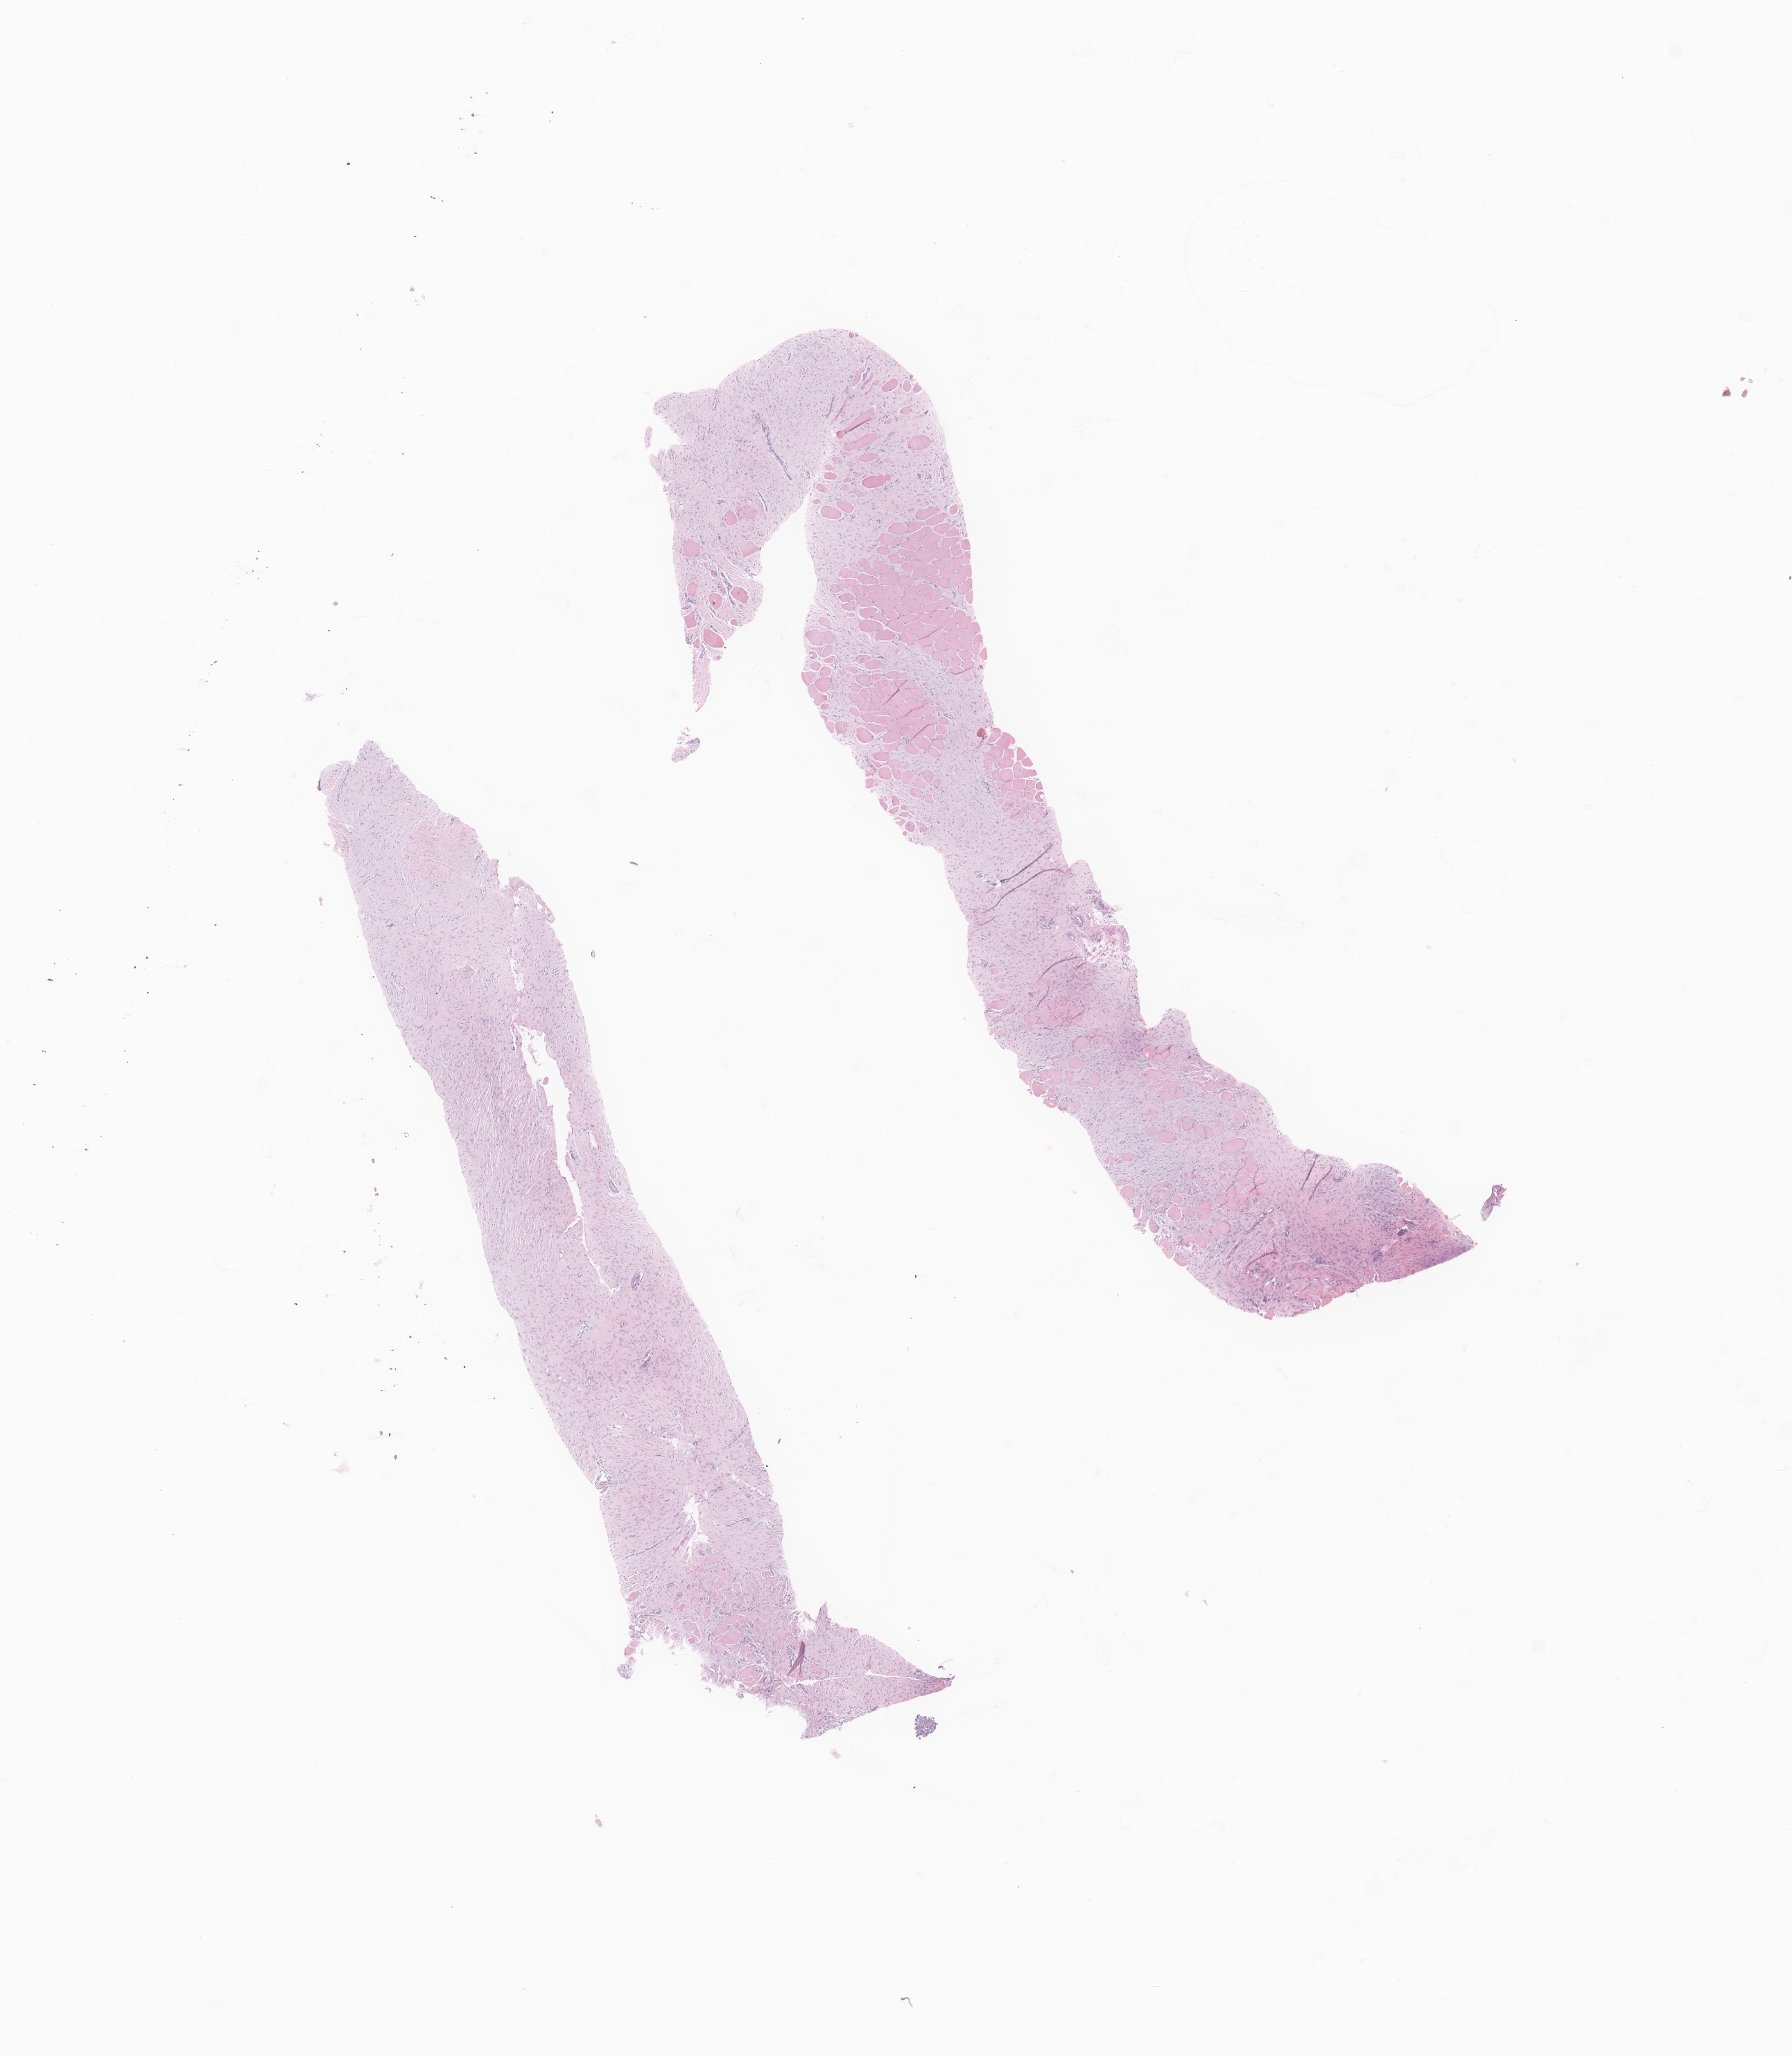
Hematoxylin and eosin (H&E) whole-slide image of tumor tissue from the soft tissue — a low-resolution overview of the entire scanned area, about 10.9 x 12.5 mm; formalin-fixed paraffin-embedded section. Patient: male, age 157 months (13 years 1 month).
Diagnosis (ICD-O-3 morphology term): Aggressive fibromatosis.